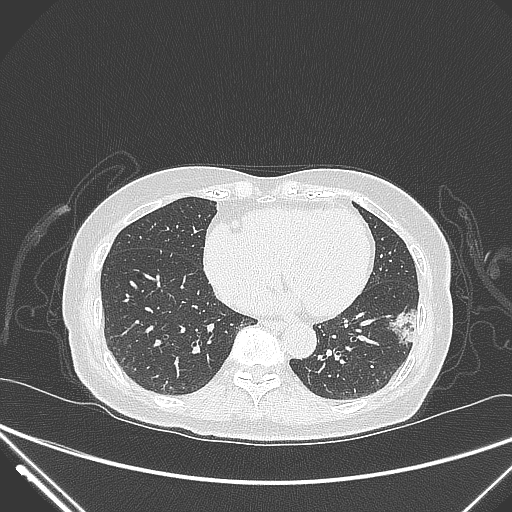
Chest CT, one axial slice. Position 108 of 310 along the scan axis. Lung window (W 1500 / L -600 HU). 1 mm slice thickness. 512 × 512 image matrix, field of view 377 × 377 mm. Patient: female, 82 years. From the clinical record (not read from this slice): clinical TNM (as recorded): T1c N0 M0; histopathological grade: G2.
Structures marked on this image (bounding box drawn by a radiologist):
- lung tumour (recorded histology: adenocarcinoma): bounding box [x1, y1, x2, y2] px = [382, 294, 426, 347]